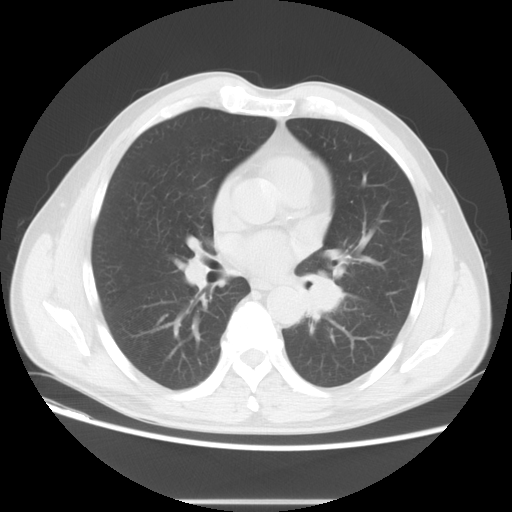
Chest CT, one axial slice; slice 29 of 59 in the series (ordered by position); reconstruction kernel STANDARD; lung window (W 1500 / L -600 HU); 5 mm slice thickness; 512 × 512 image matrix, field of view 378 × 378 mm. Patient: male, 59 years. From the clinical record (not read from this slice): clinical TNM (as recorded): T2 N3 M0.
Structures marked on this image (bounding box drawn by a radiologist):
- lung tumour (recorded histology: small cell carcinoma): bounding box (x1, y1, x2, y2) in pixels: (297, 269, 348, 335)